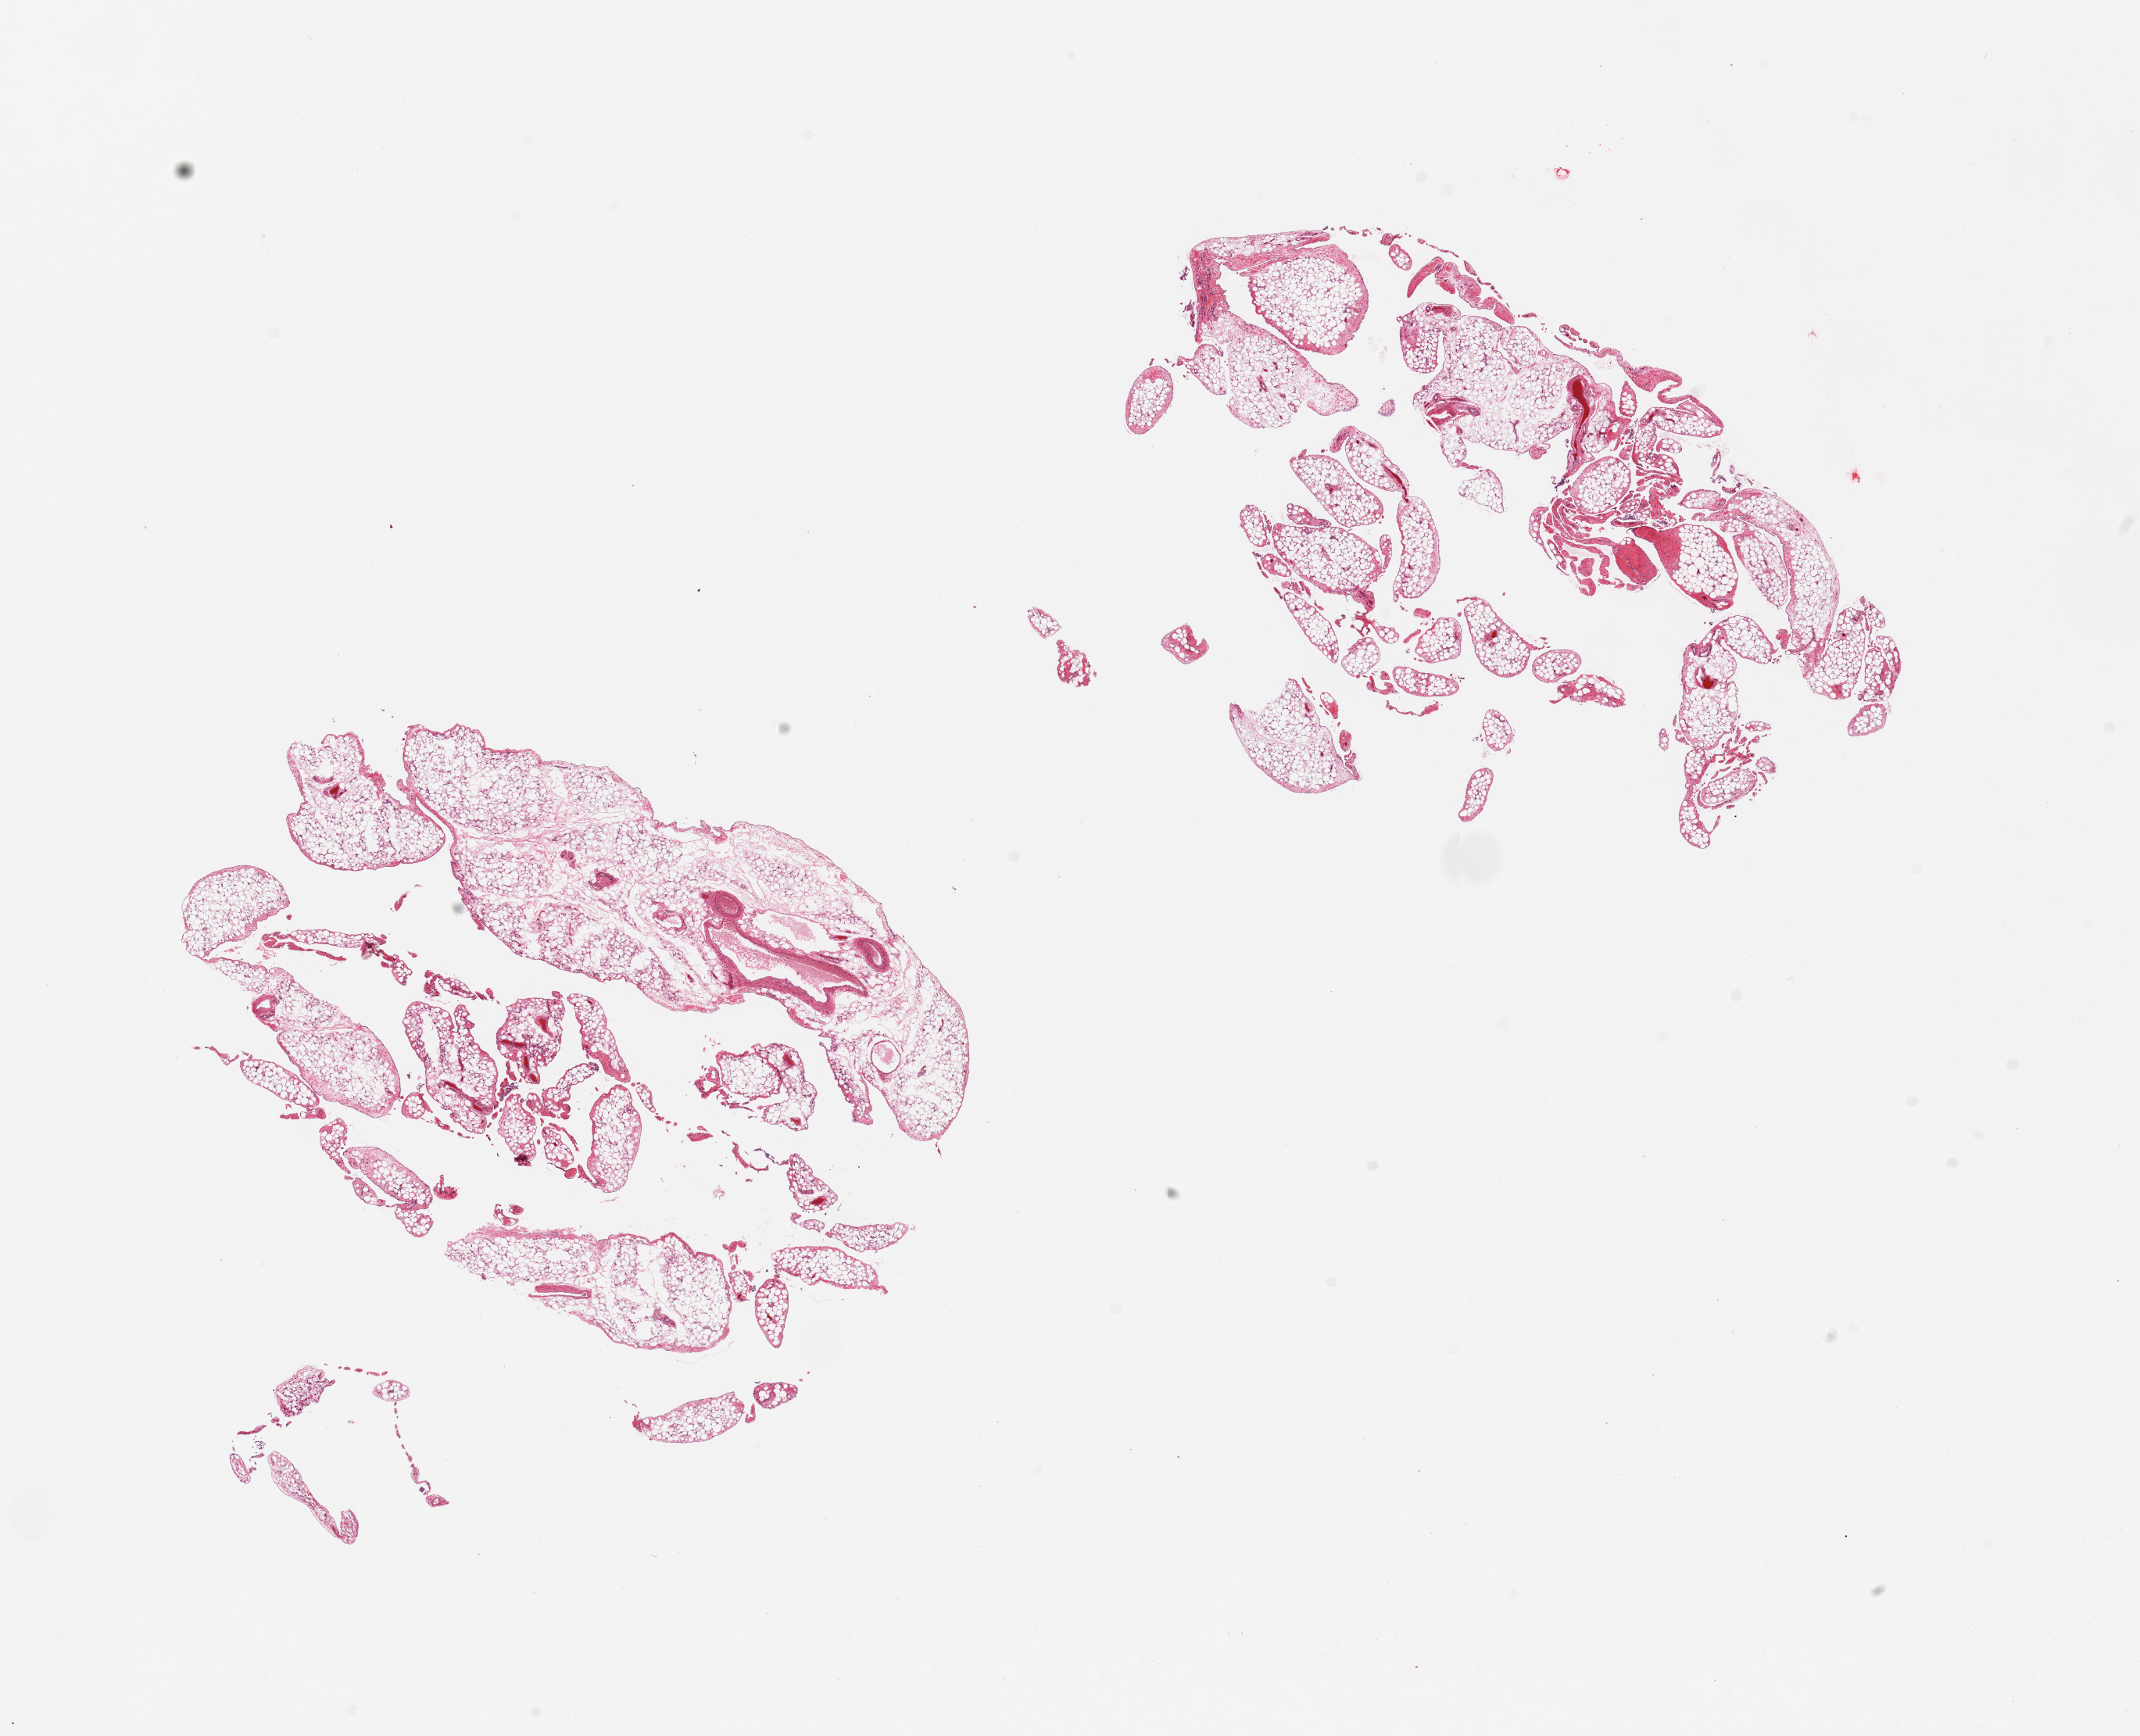
H&E whole-slide image, brightfield — low-resolution overview of the scanned area, about 21.7 x 17.6 mm. PAXgene-fixed paraffin-embedded (PFPE) section. Target tissue: omentum. Donor tissue sample. Donor: male.
Reviewer comment on this tissue sample: 2 pieces, no significant fascia/vascular tissue.